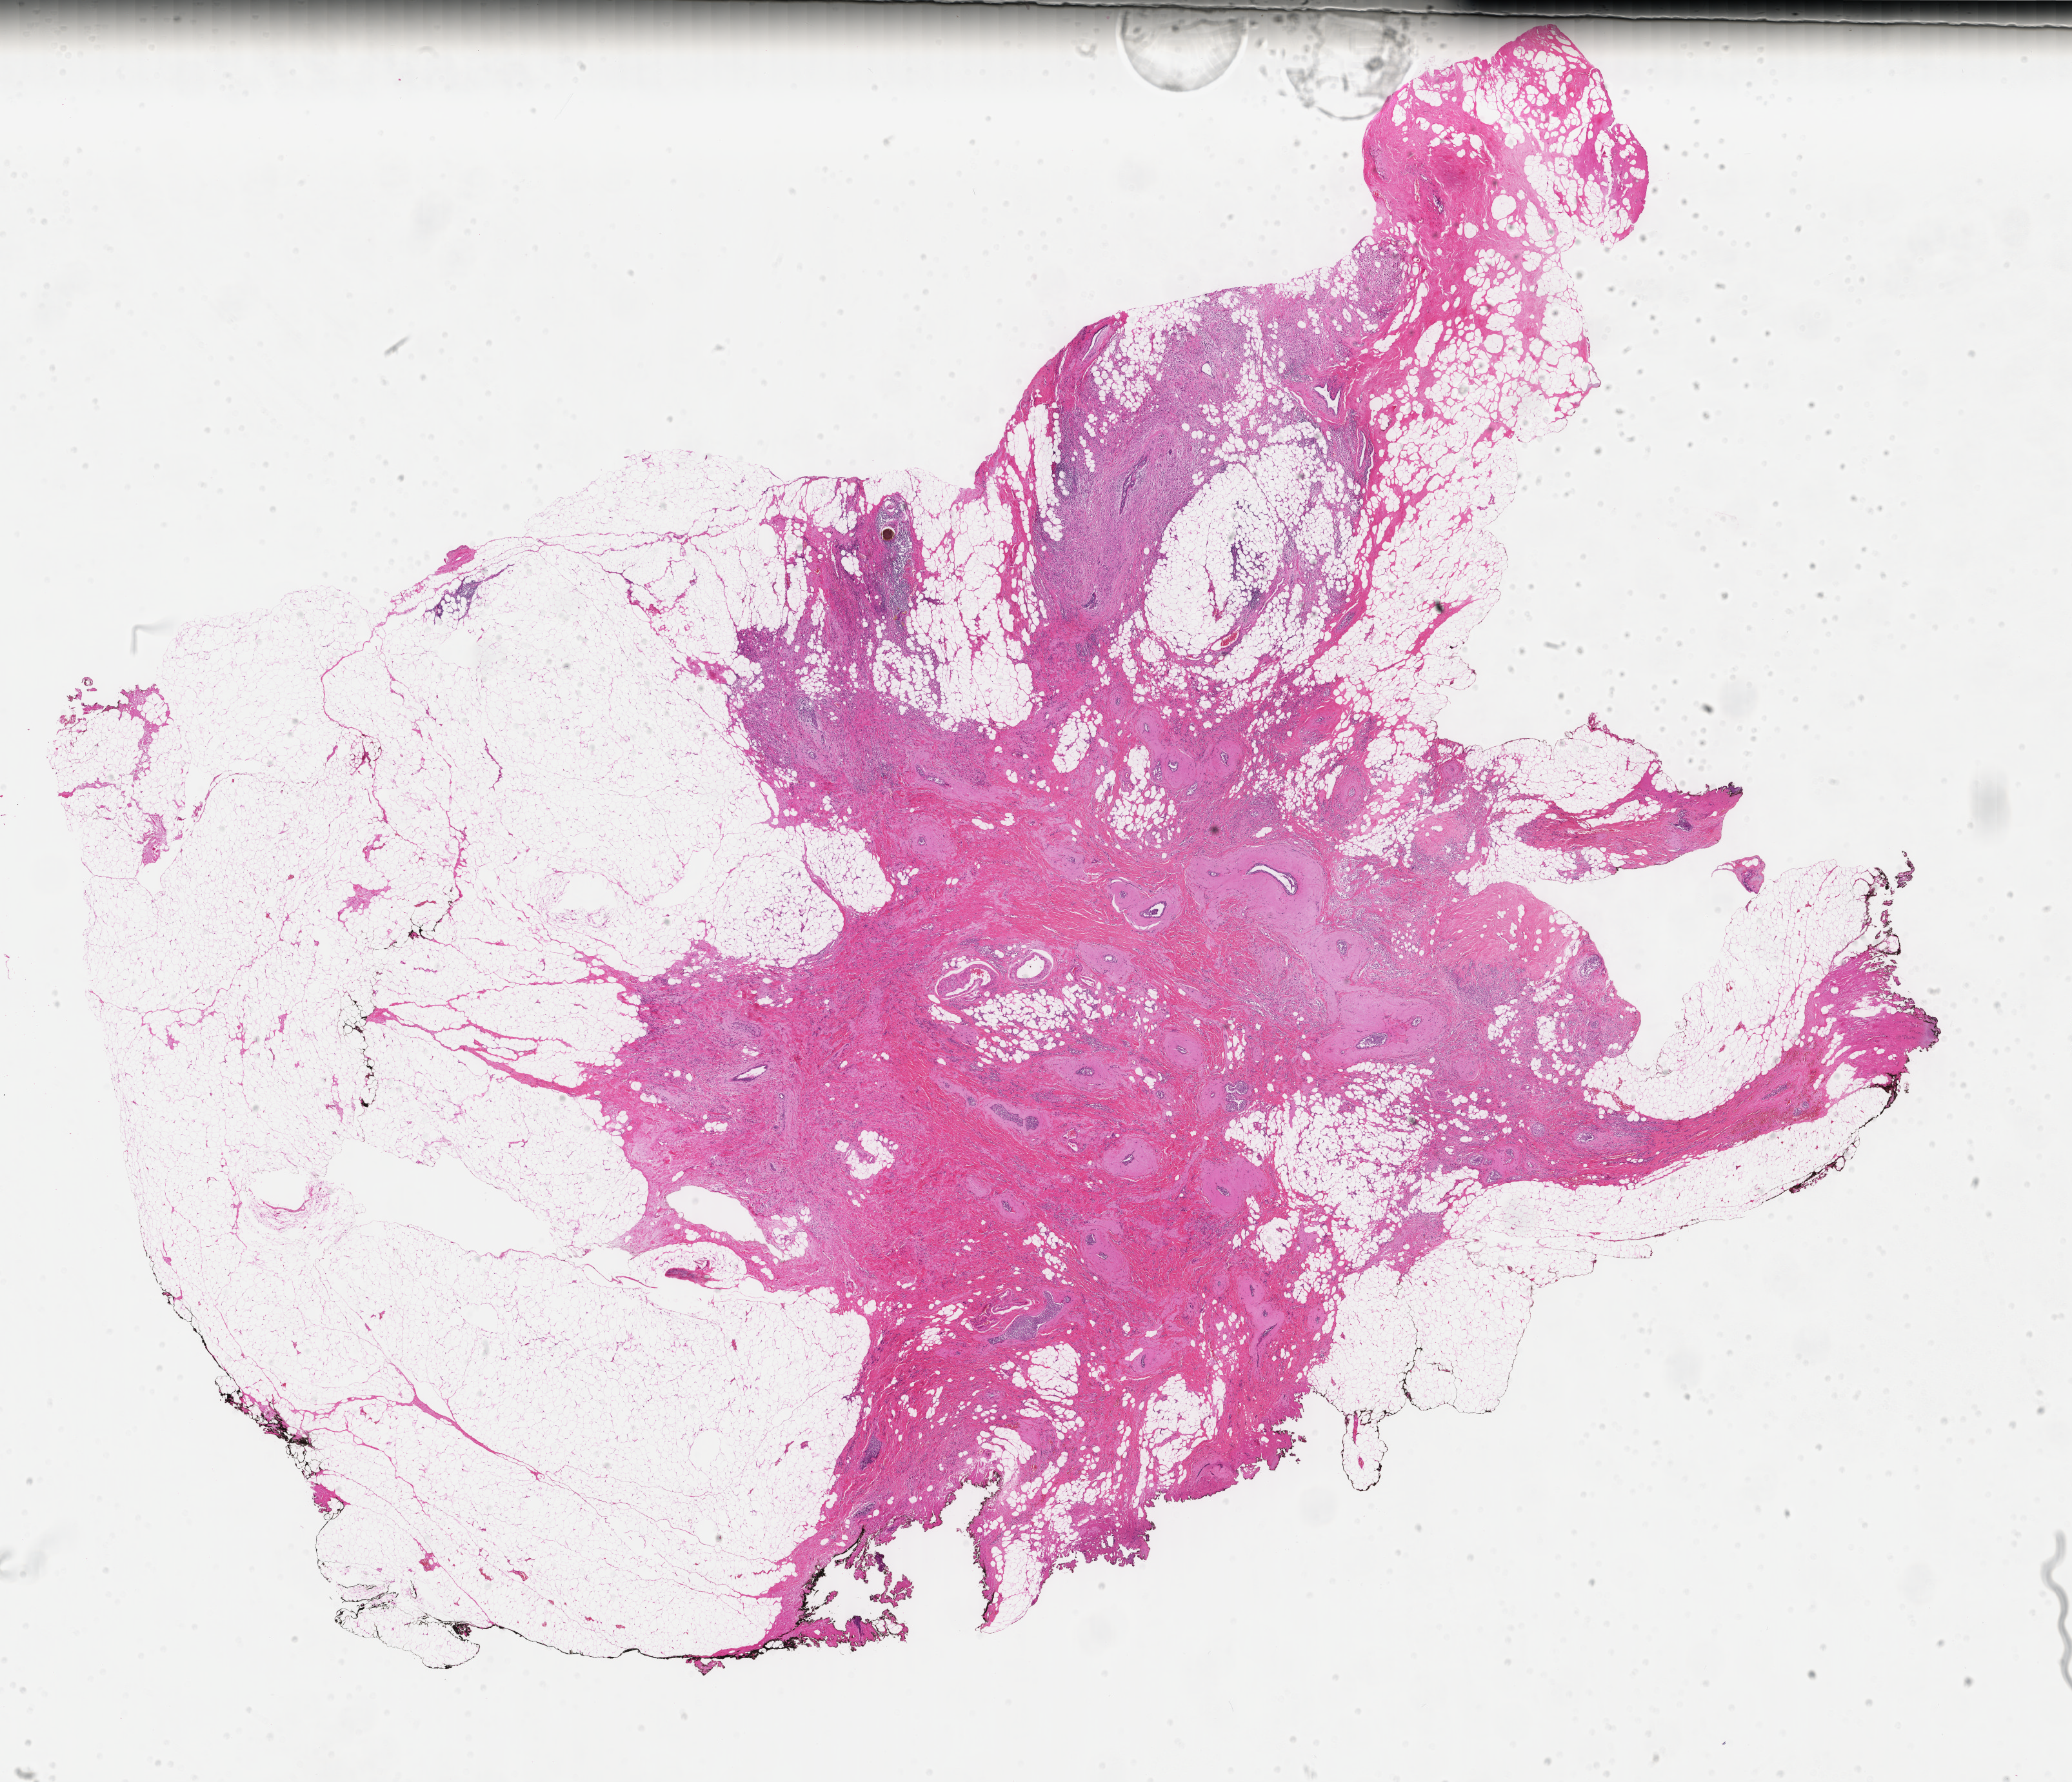
H&E-stained whole-slide image, whole scanned area (about 25.5 x 21.9 mm) shown as a low-resolution overview; formalin-fixed paraffin-embedded (FFPE) diagnostic section; primary tumour sample from the breast. Female patient; age at initial diagnosis 70 years.
AJCC pathologic stage: IIA (6th edition). Histologic diagnosis: Lobular carcinoma, NOS. Lymph nodes positive (case pathology): 0 of 4 examined.